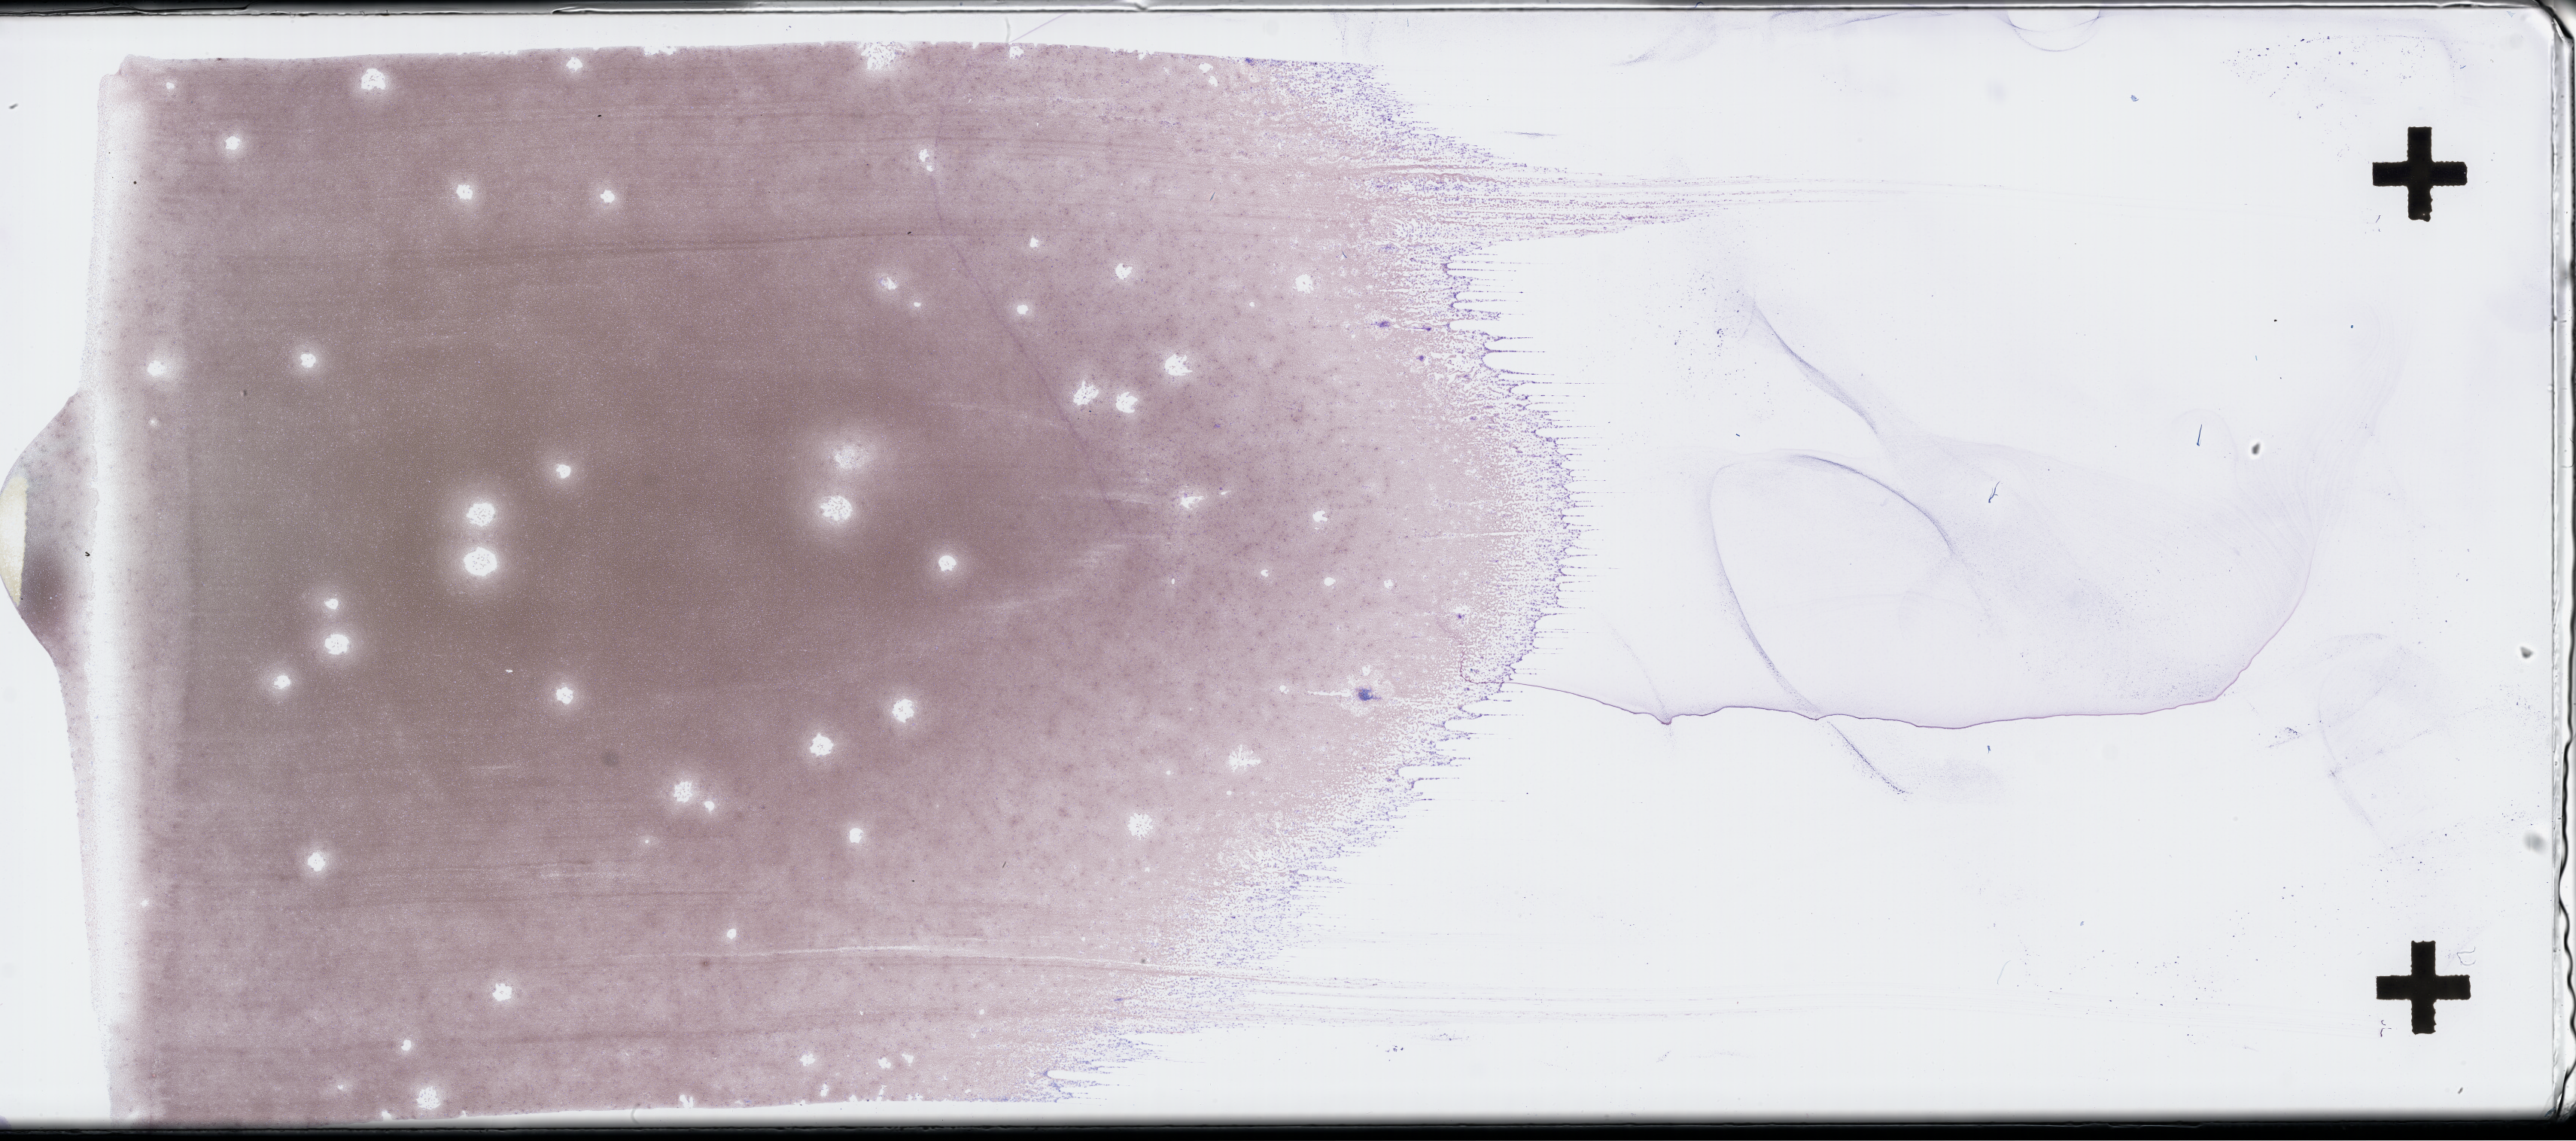
Whole-slide image of a bone marrow smear, Wright-Giemsa stain — whole scanned area (about 55.3 x 24.5 mm) shown as a low-resolution overview, EDTA-anticoagulated smear, collected on treatment. Patient: male.
From a patient with: Plasma Cell Myeloma.